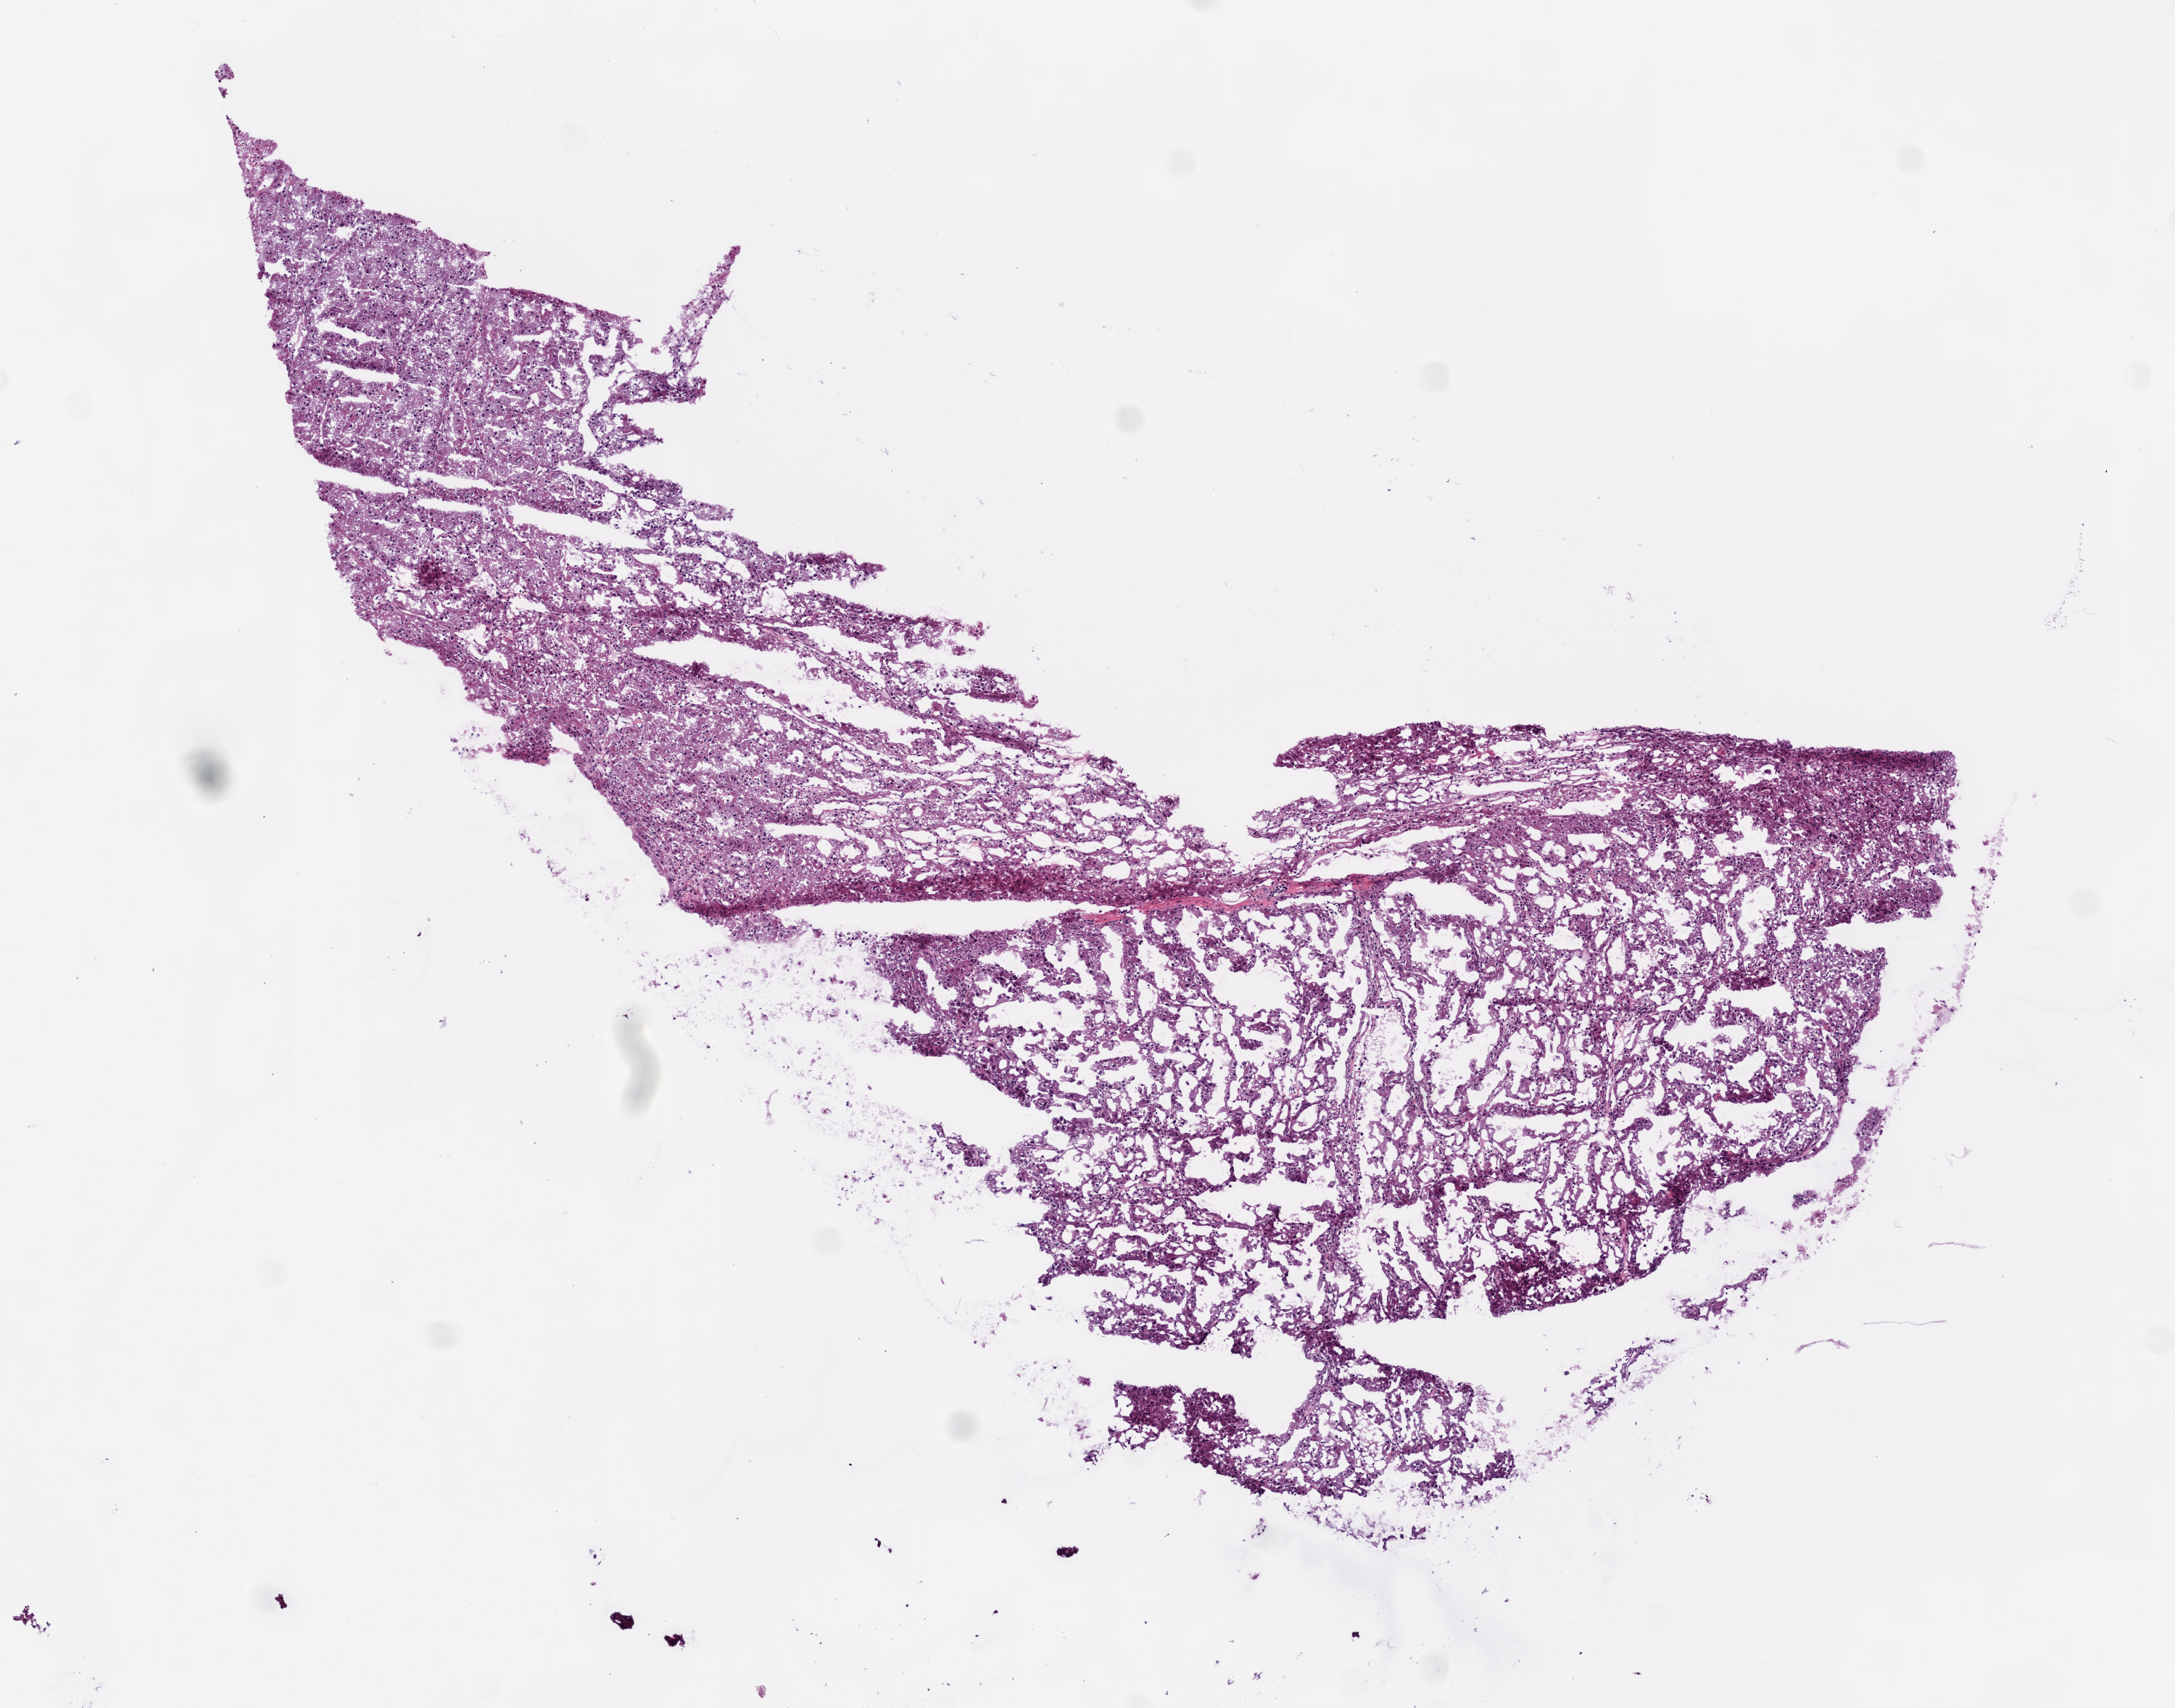
H&E-stained whole-slide image, low-resolution overview of the scanned area, about 6.0 x 4.7 mm, frozen section from the bottom of the tissue portion, sample: primary tumour, kidney. Male patient; age at initial diagnosis 48 years. Histologic grade: G3 (poorly differentiated). Slide review estimates, as recorded: tumour cells 82%, tumour nuclei 80%, normal cells 0%, stromal cells 10%, necrosis 8%.
Laterality: left. Pathologic diagnosis: Clear cell adenocarcinoma, NOS. AJCC pathologic stage: II (6th edition). Lymph nodes positive (case pathology): 0 of 16 examined.